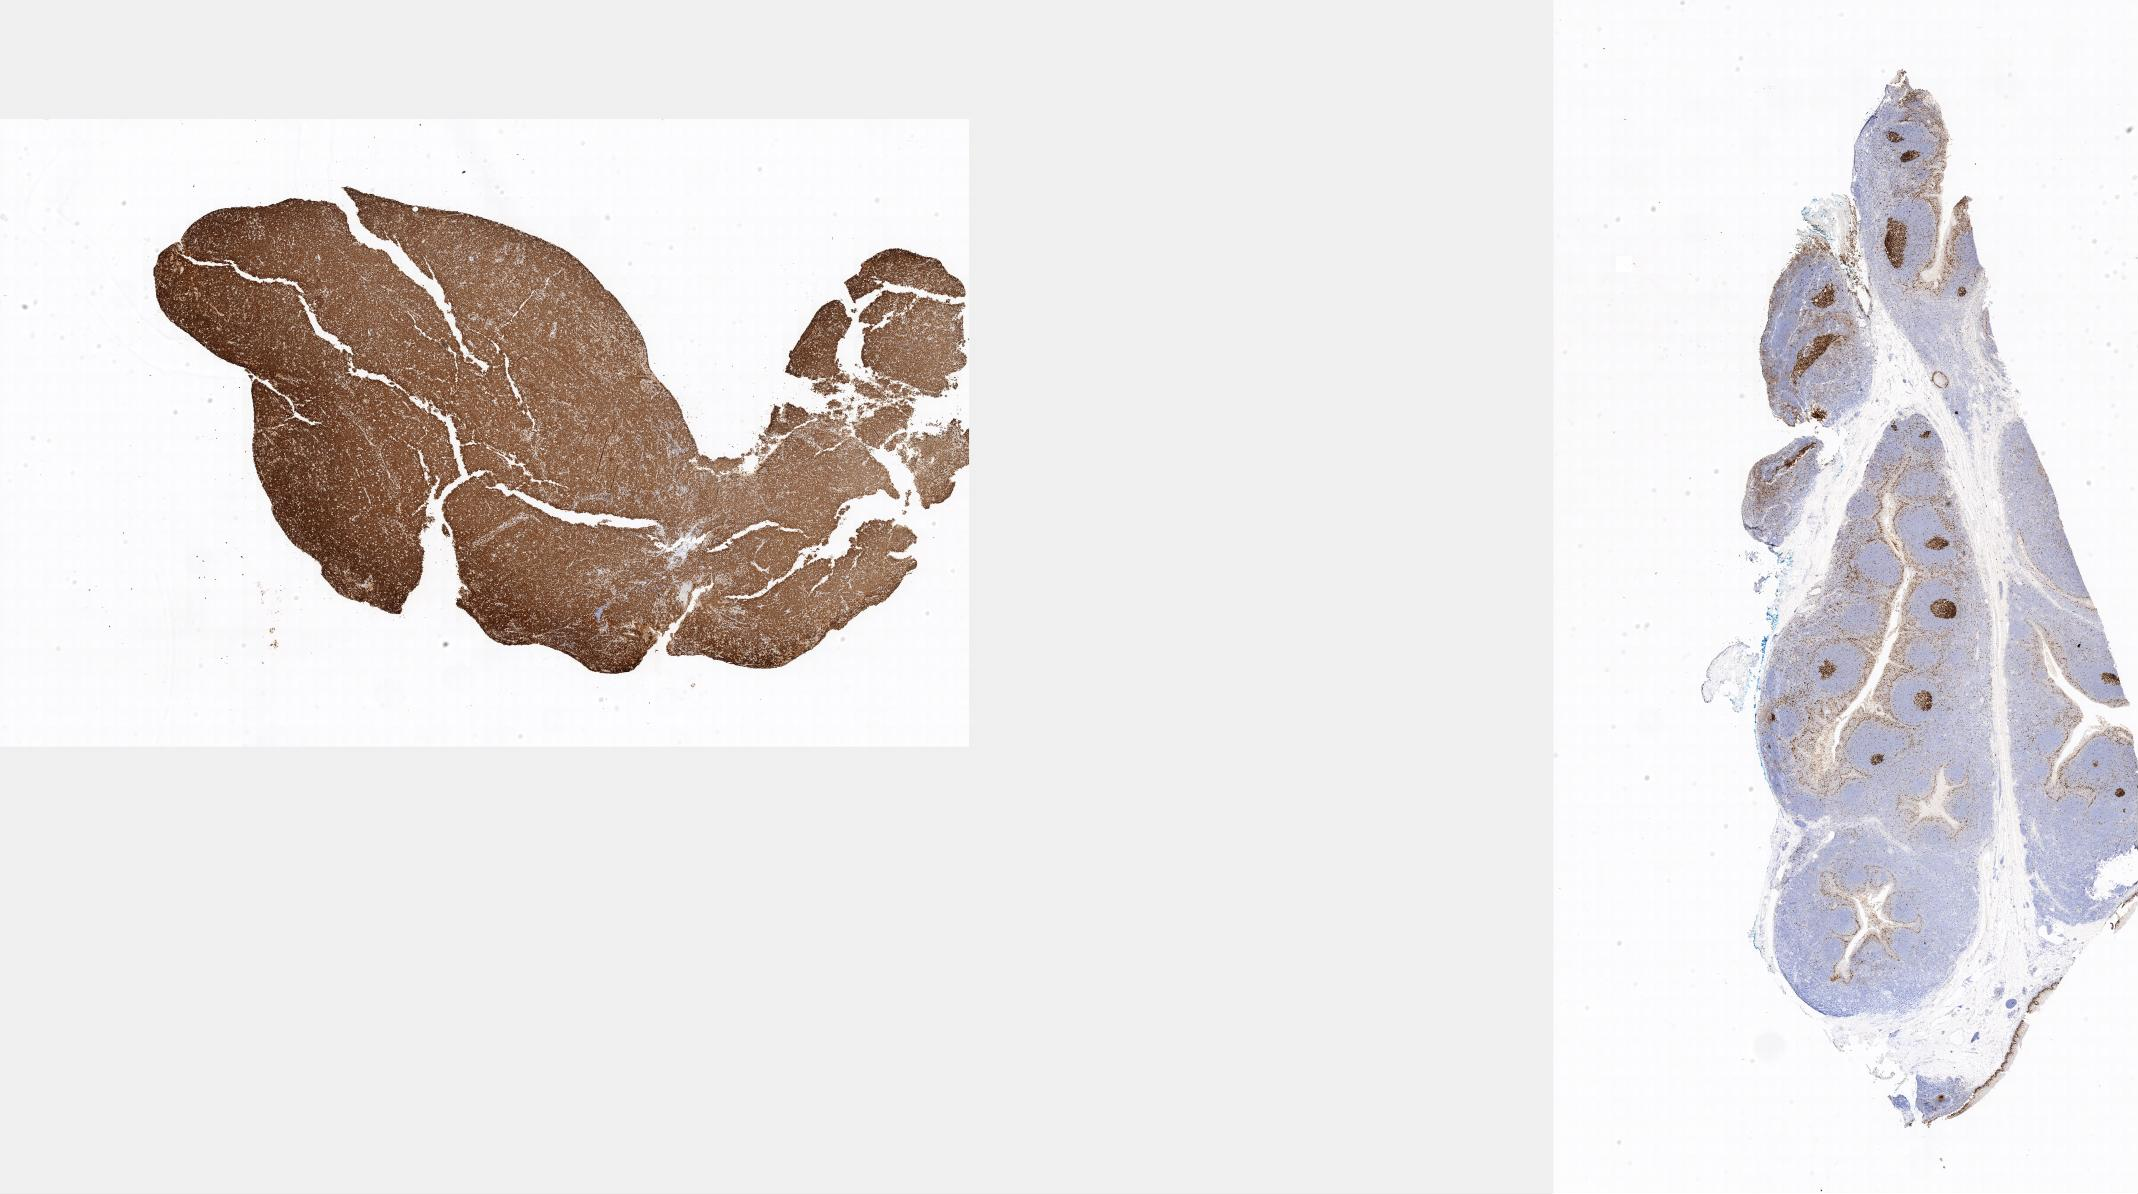
Whole-slide image, immunohistochemical stain for Ki-67, shown as a low-resolution overview of the whole scanned area, specimen: tumor tissue, site: lymph node of head and neck. Patient: male, age at initial diagnosis 5 years.
Histologic diagnosis: Burkitt lymphoma, NOS.